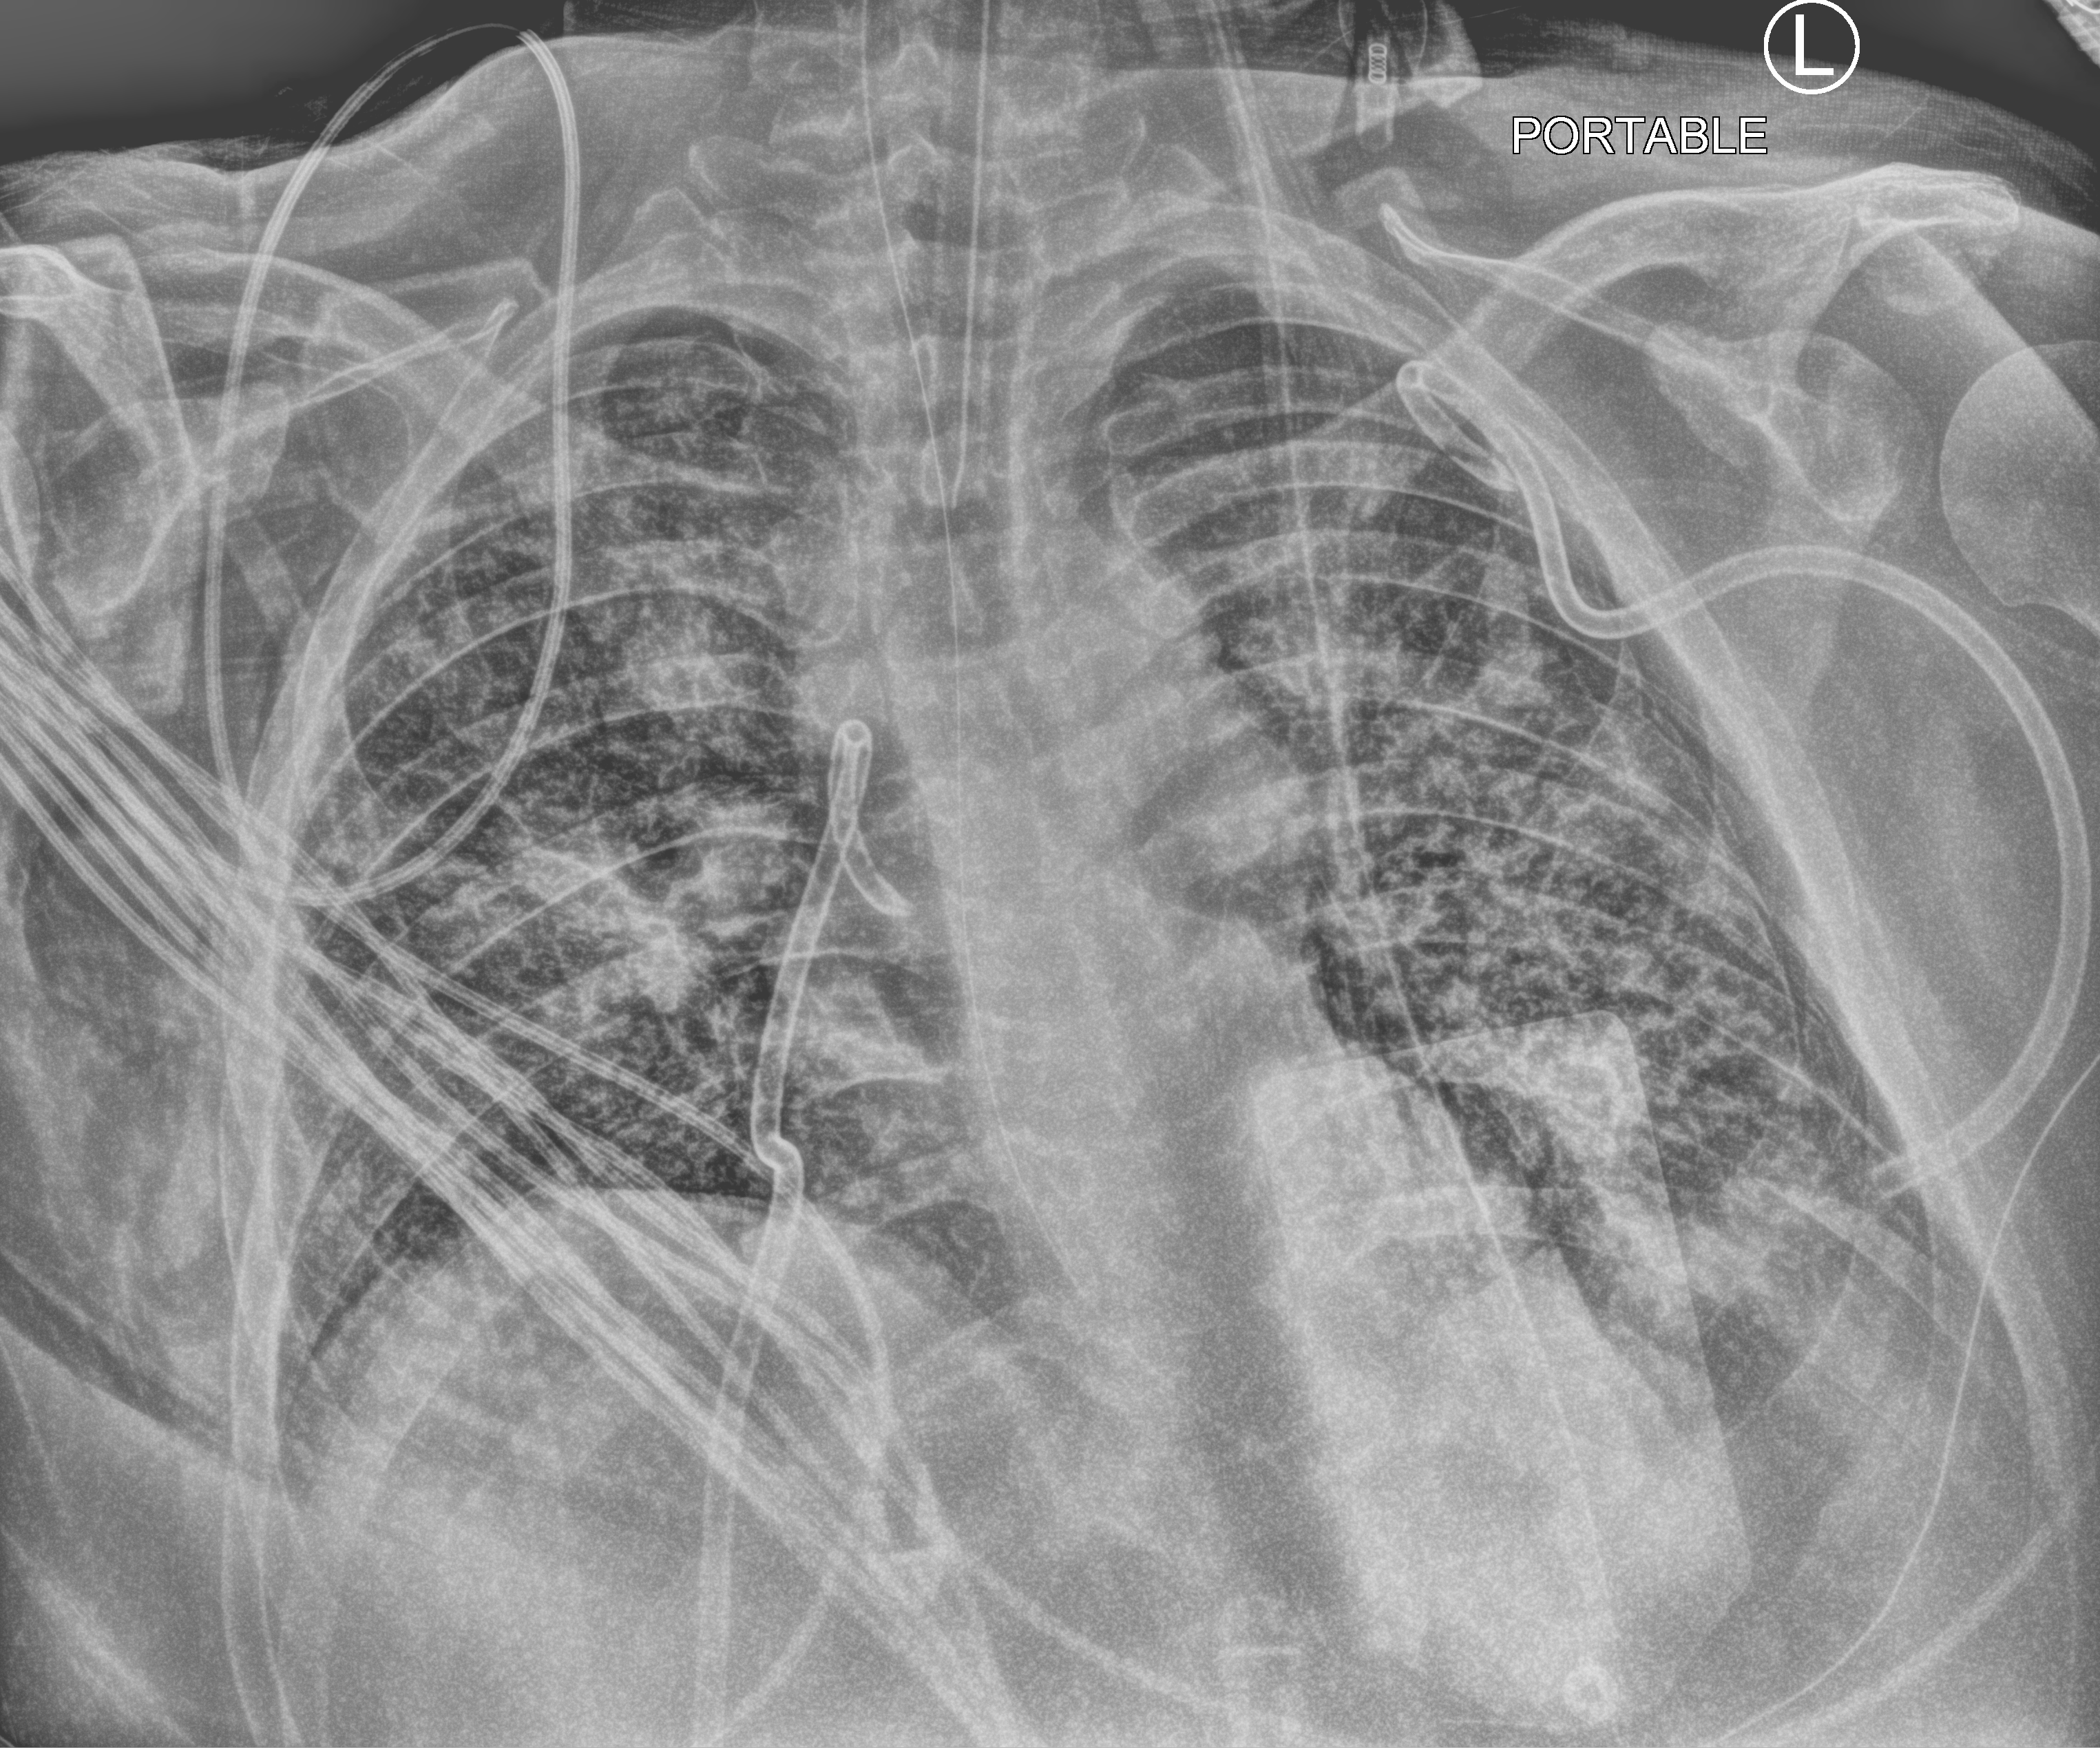
Chest X-ray (portable), anteroposterior (AP) projection. Patient hospitalised with COVID-19, aged 18–59 years.
Hospital-stay facts (about this admission, not read from this image; timing relative to this image not recorded): admitted to intensive care during this hospital stay: yes.